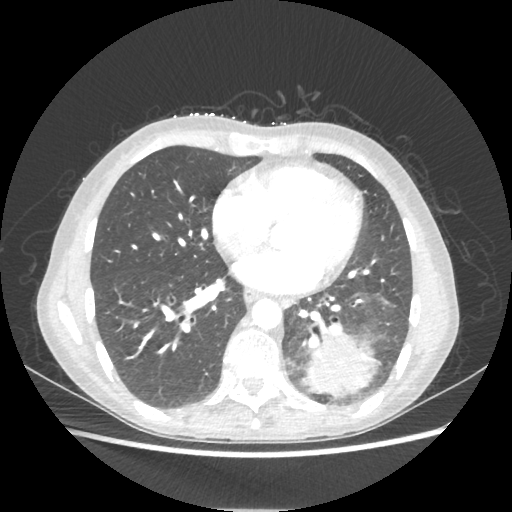
Chest CT, one axial slice. Position 88 of 221 along the scan axis. Reconstruction kernel STANDARD. 80 kVp. Lung window (W 1500 / L -600 HU). 512 × 512 image matrix. Female patient, age 53 years. Case-level facts recorded for this patient, not image findings: clinical TNM (as recorded): T3 N0 M0.
Outlined on this slice (bounding box drawn by a radiologist):
- lung tumour (recorded histology: adenocarcinoma): bounding box <305,332,378,399> (left, top, right, bottom; pixels)